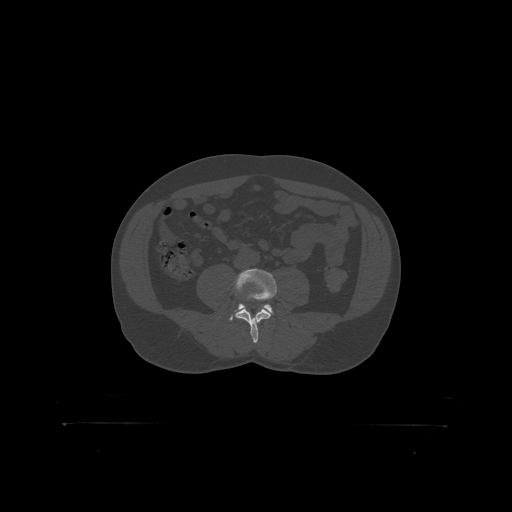
CT including the spine, one axial slice. Reconstruction kernel STANDARD. 120 kVp. Bone window (W 1800 / L 400 HU). 1.25 mm slice thickness. 512 × 512 image matrix, field of view 650 × 650 mm. Patient: male, 46 years. From the clinical record (not read from this slice): primary cancer: skin.
Outlined on this slice (semi-automatic segmentation, software-assisted and operator-edited):
- L4 vertebra: box from (x=234, y=270) to (x=277, y=319) px
- L5 vertebra: (x=237, y=304)–(x=274, y=314)